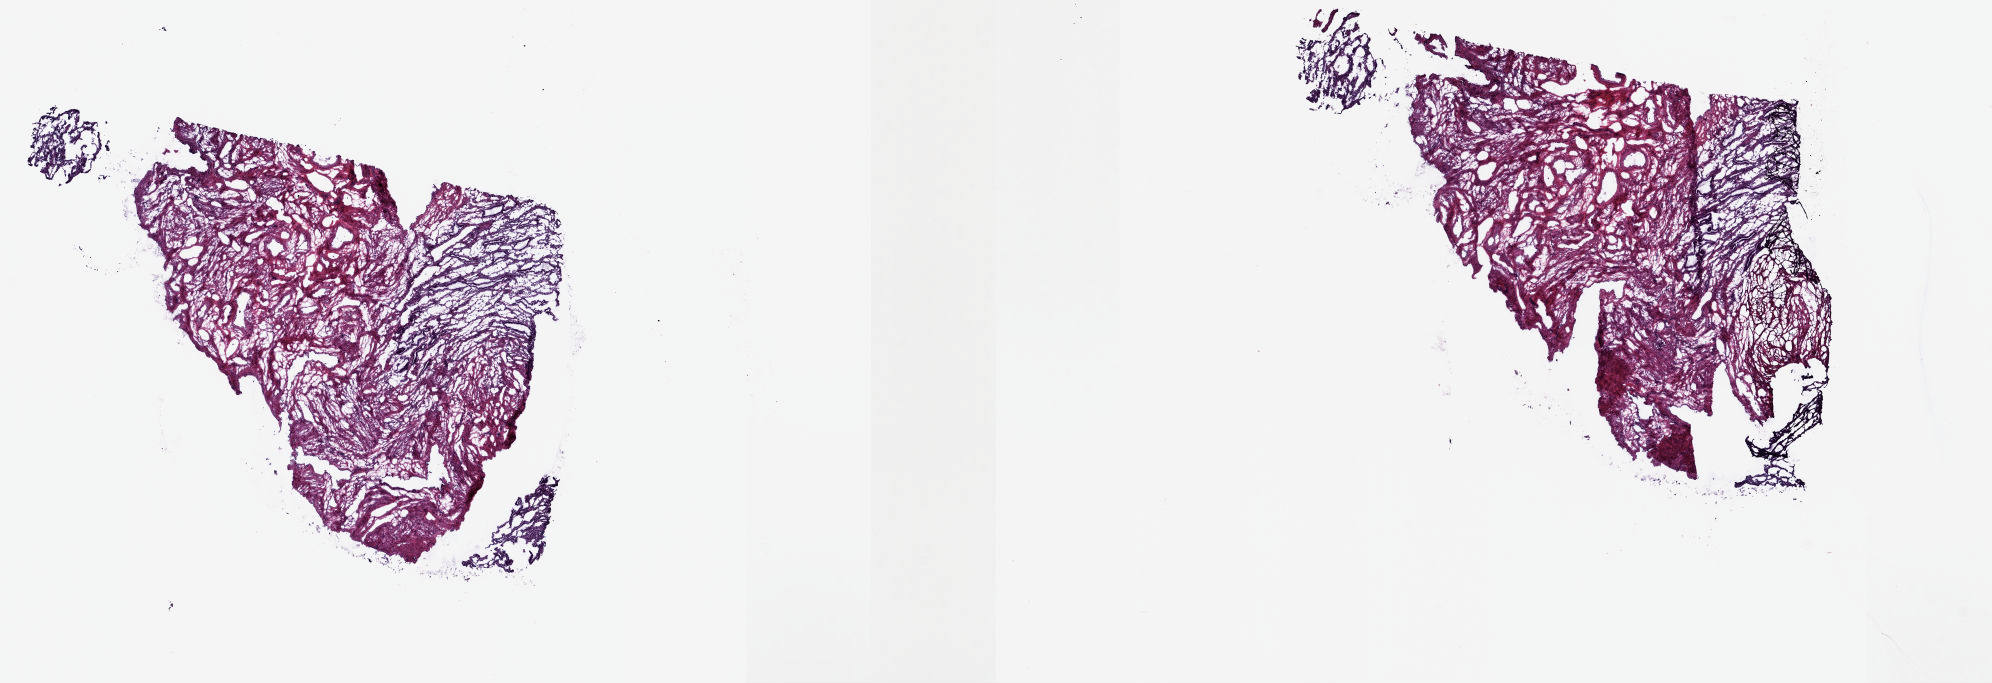
Whole-slide histology image, H&E, whole scanned area (about 15.8 x 5.4 mm) shown as a low-resolution overview. Frozen section. Solid tissue normal (non-tumour tissue) sample from the uterus. Pathologist review of this section (percent, as recorded): tumour cells 0%, normal cells 100%.
This section: solid tissue normal sample (biorepository sample class).